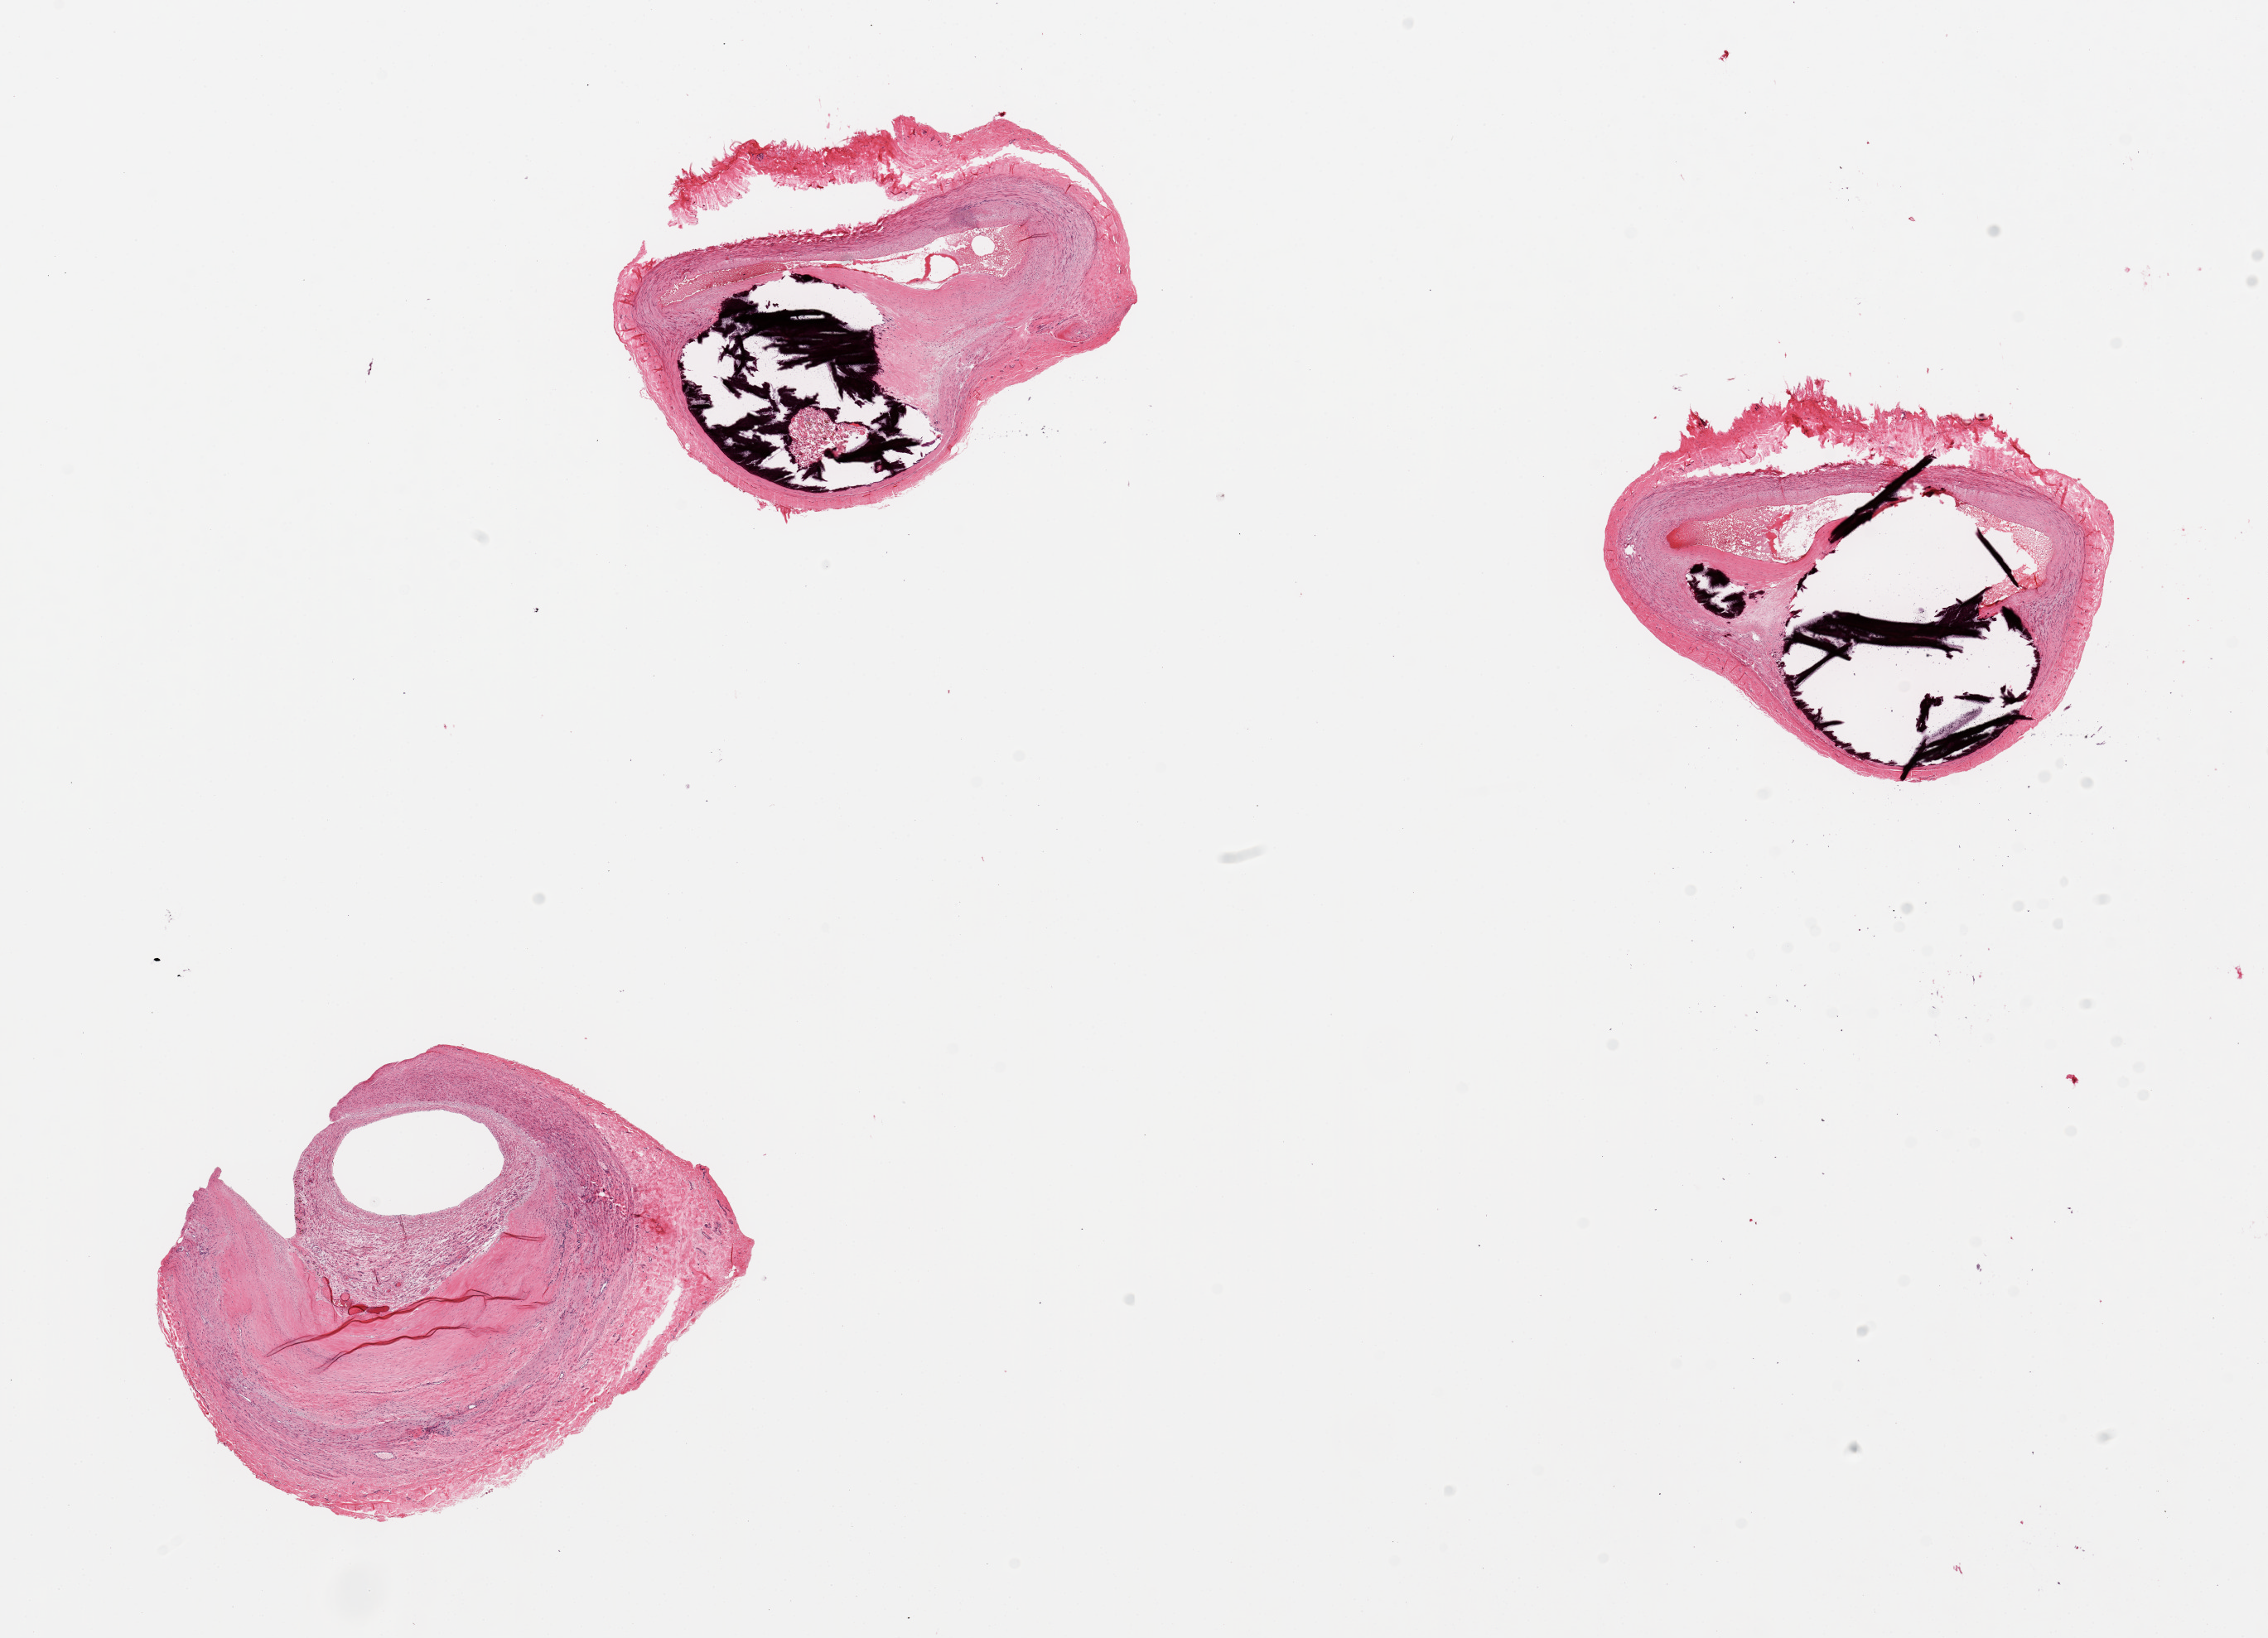
Digitized hematoxylin and eosin (H&E)-stained section, whole scanned area (about 21.7 x 15.6 mm, from a 20x scan) shown as a low-resolution overview. PAXgene-fixed, paraffin-embedded tissue. Target tissue: tibial artery. Donor tissue sample. Donor sex: male.
- review note (as recorded): 3 pieces; severe calcific atherosclerosis with profound narrowing of the lumen